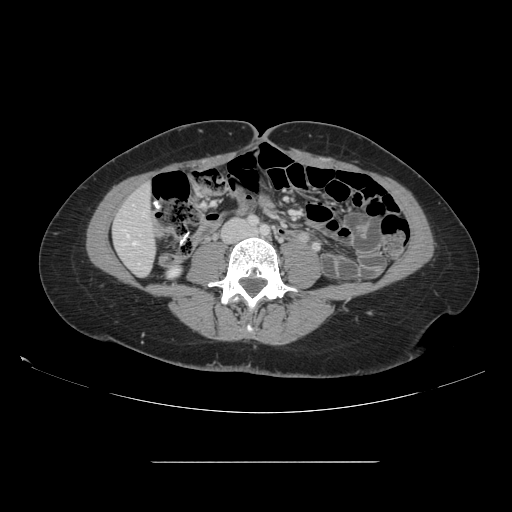
Contrast-enhanced abdominal CT, one axial slice. Intravenous contrast given. Soft-tissue window (W 400 / L 40 HU). 2.5 mm slice thickness. 512 × 512 image matrix. Female patient, age 46 years. From the clinical record (not read from this slice): diagnosis: colorectal cancer liver metastases, imaged before liver resection; multiple liver metastases: yes; largest metastasis: 3 cm; disease in both lobes: yes.
Outlined on this slice (manually delineated by an expert):
- liver: bounding box (x1, y1, x2, y2) in pixels: (114, 187, 156, 275)
- planned liver remnant (the part of the liver to remain after resection): (114, 187, 156, 275)